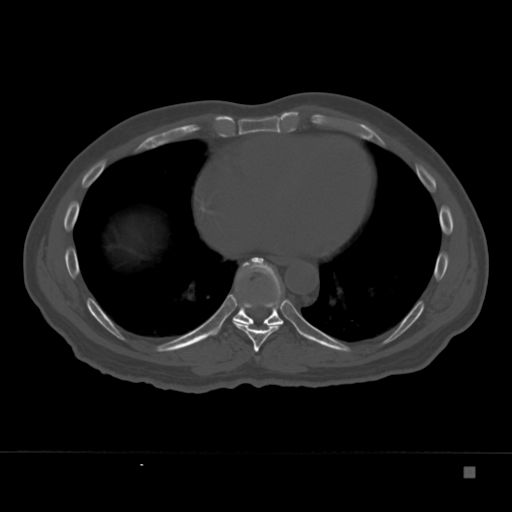
CT including the spine, one axial slice; slice 199 of 332 in the series (ordered by position); reconstruction kernel Br40s; 120 kVp; bone window (W 1800 / L 400 HU); 512 × 512 image matrix. Patient: male, 72 years. From the clinical record (not read from this slice): primary cancer: skeletal.
Structures marked on this image (semi-automatically segmented with operator editing):
- T8 vertebra: box from (x=233, y=321) to (x=280, y=352) px
- T9 vertebra: (x=213, y=257)–(x=285, y=335)